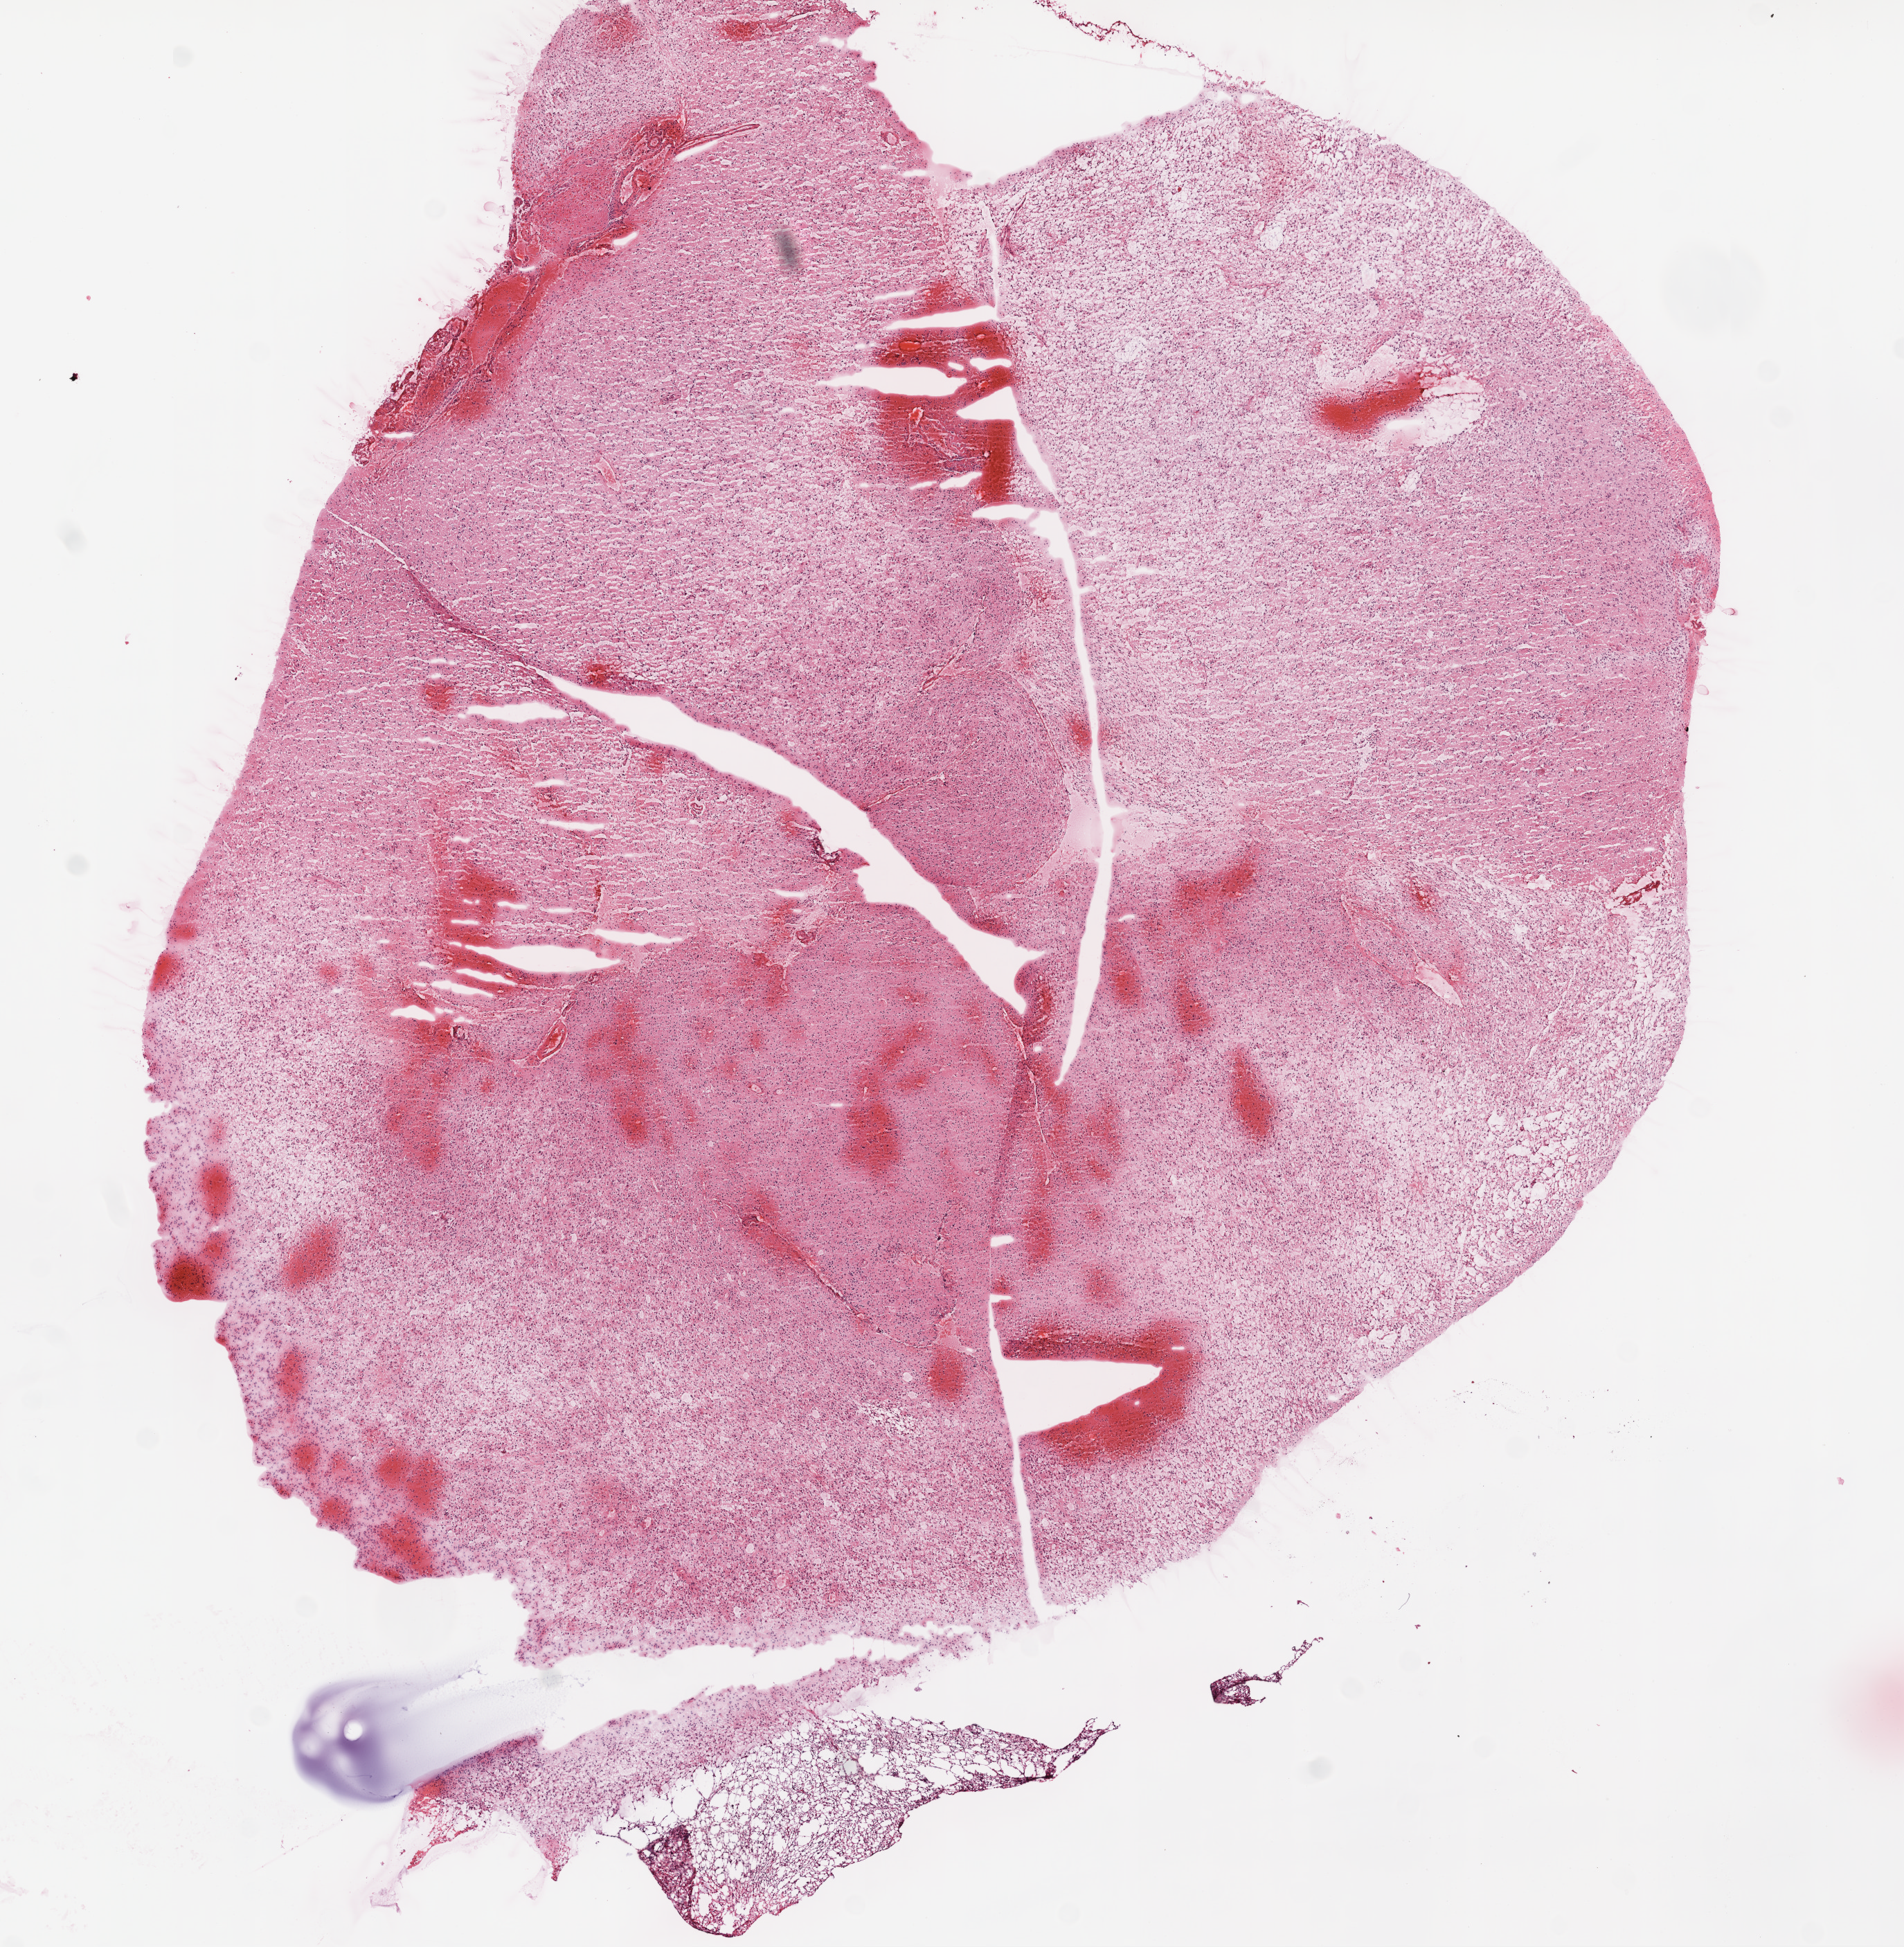
Whole-slide histology image, Hematoxylin and eosin (H&E) stained, shown as a low-resolution overview of the whole scanned area (about 11.0 x 11.3 mm, from a 20x scan). Frozen section from the top of the tissue portion. Sample: primary tumour, brain. Male patient; age at initial diagnosis 34 years. Histologic grade: G3 (poorly differentiated). Pathologist review of this section (percent, as recorded): tumour cells 100%, tumour nuclei 65%, normal cells 0%, stromal cells 0%, necrosis 0%.
Pathologic diagnosis: Astrocytoma, anaplastic. Laterality: right.